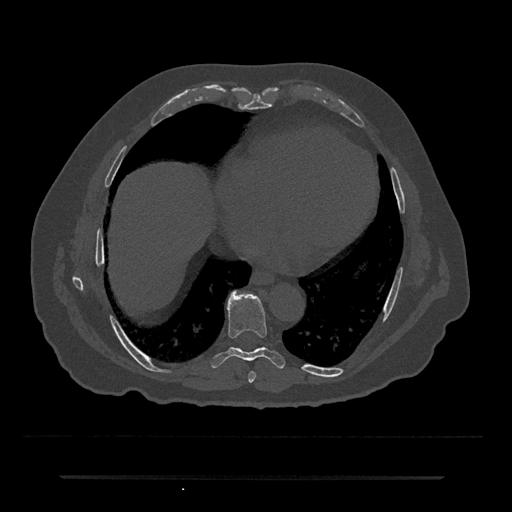
CT including the spine, one axial slice. Position 331 of 797 along the scan axis. Reconstruction kernel Br40s/3. 120 kVp. Bone window (W 1800 / L 400 HU). 0.5 mm slice thickness. 512 × 512 image matrix, field of view 437 × 437 mm. Patient: male, 69 years. From the clinical record (not read from this slice): primary cancer: prostate.
Structures marked on this image (semi-automatically segmented with operator editing):
- T7 vertebra: box from (x=248, y=371) to (x=256, y=383) px
- T8 vertebra: (x=211, y=291)–(x=285, y=369)